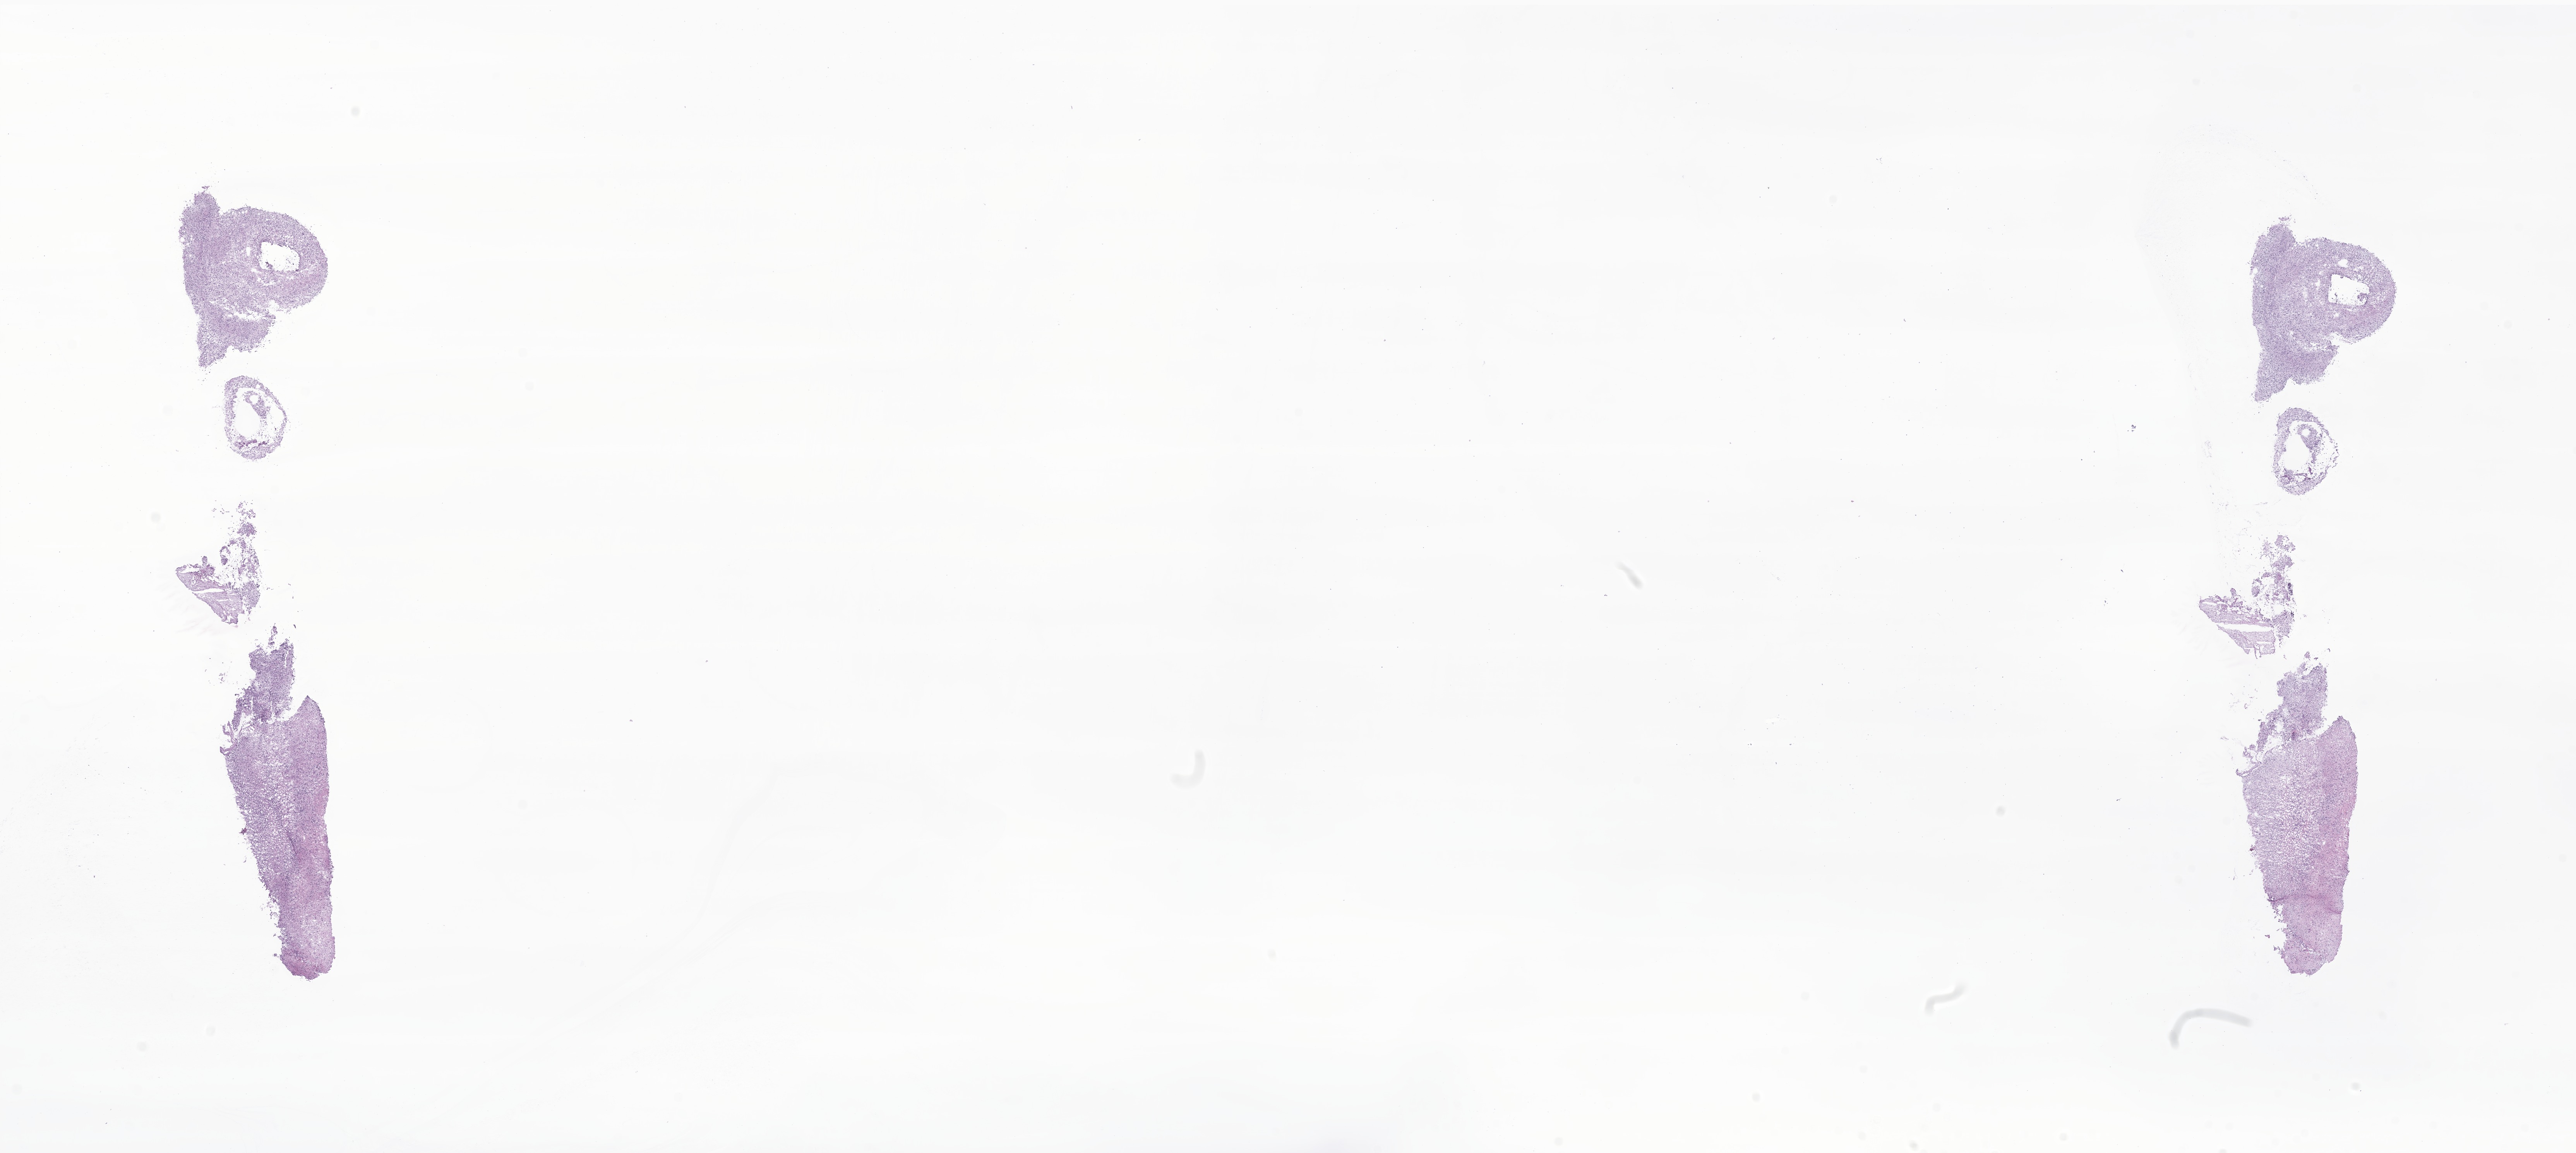
H&E whole-slide image of tumor tissue from the cerebellum — low-resolution overview of the scanned area, about 28.1 x 12.6 mm; cryosection (OCT / tissue freezing medium). Patient male; age 131 months (10 years 11 months).
Diagnosis: Large cell medulloblastoma.